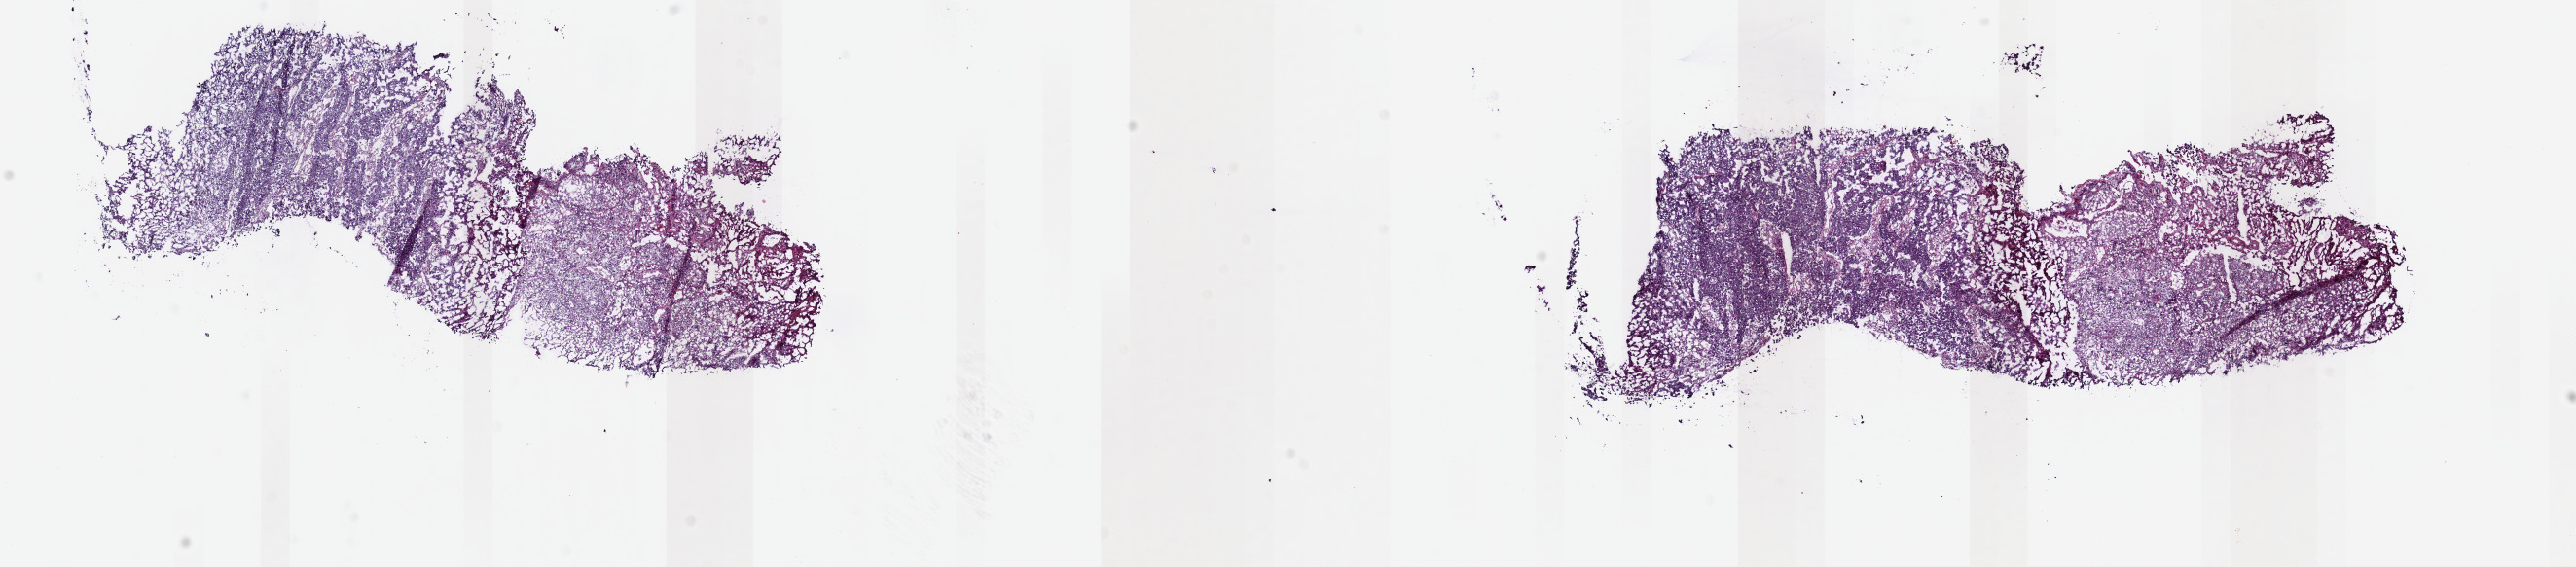
Whole-slide histology image, Hematoxylin and eosin (H&E) stained — whole scanned area (about 20.9 x 4.6 mm, slide scanned at 40x) shown as a low-resolution overview, frozen section from the top of the tissue portion, sample: primary tumour, bladder. Male, age 67 years at initial diagnosis. Histologic grade: high grade. Composition of this section per pathologist review: tumour cells 85%, tumour nuclei 80%, normal cells 0%, stromal cells 0%, necrosis 15%. Inflammatory infiltration, as recorded: lymphocyte infiltration 8%, monocyte infiltration 1%, neutrophil infiltration 1%.
AJCC pathologic stage: II (7th edition). Pathologic diagnosis: Transitional cell carcinoma (trigone of bladder).